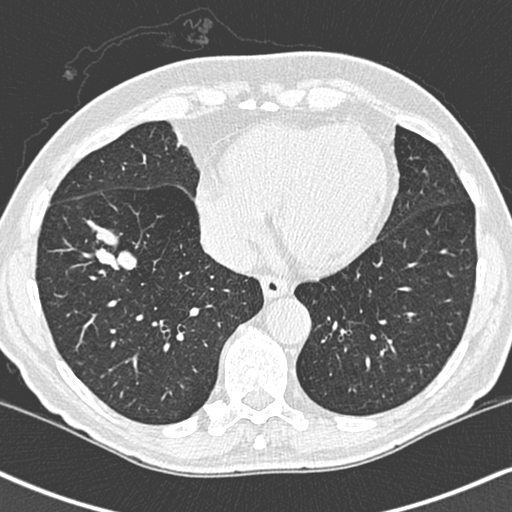
Low-dose screening chest CT, one axial slice. Position 90 of 248 along the scan axis. Lung window (W 1500 / L -600 HU). 1.3 mm slice thickness. 512 × 512 image matrix.
Structures marked on this image (manually delineated by an expert):
- lesion 1 (tumor, lower lobe of right lung): bounding box <86,182,137,232> (left, top, right, bottom; pixels)